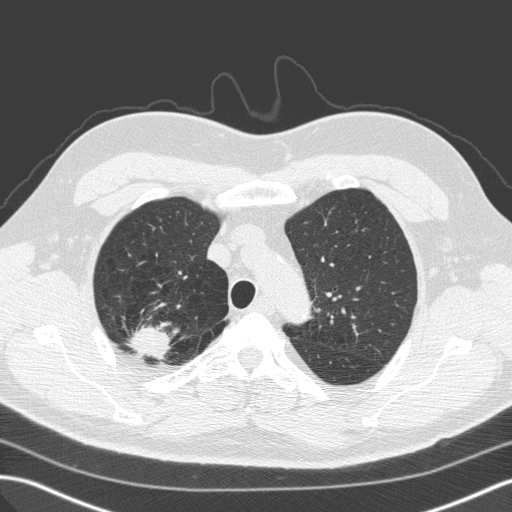
Low-dose screening chest CT, one axial slice; slice 122 of 149 in the series (ordered by position); 120 kVp; lung window (W 1500 / L -600 HU); 512 × 512 image matrix, field of view 357 × 357 mm.
Outlined on this slice (expert manual segmentation):
- lesion 1 (tumor, upper lobe of right lung): bounding box (x1, y1, x2, y2) in pixels: (128, 326, 172, 360)